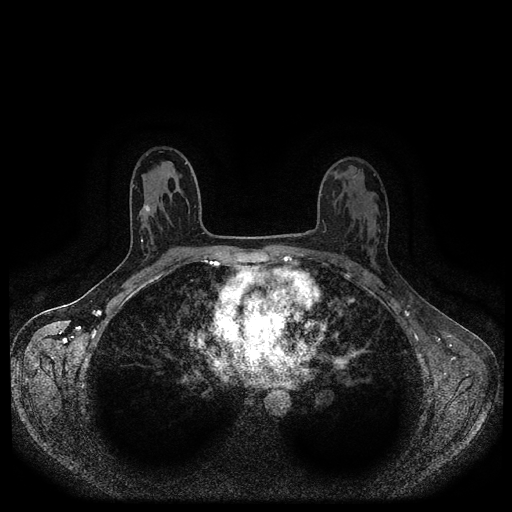
Breast MRI (dynamic contrast-enhanced, multi-phase), one axial slice; position 57 of 116 along the scan axis; dynamic contrast-enhanced series, time point 2 of 5 at this slice position (early post-contrast); 1.5 T; TE 2.6 ms, TR 5.4 ms; 2 mm slice thickness; 512 × 512 image matrix. Female patient, age 30 years.
Structures marked on this image (semi-automatically segmented with operator editing):
- breast lesion (labelled benign in the annotation): bounding box [x1, y1, x2, y2] px = [142, 204, 151, 214]